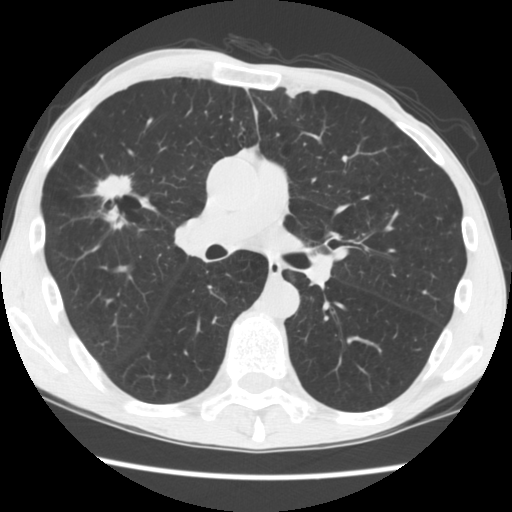
Axial slice from a low-dose chest CT screening exam. Second annual screen. Lung window (W 1500 / L -600 HU). Standard (soft-tissue) reconstruction kernel (STANDARD). 512 × 512 image matrix. Male participant, aged 56 years at enrolment. Current smoker at enrolment.
Expert-annotated lung lesion, bounding box (x1, y1, x2, y2) in pixels: (86, 164, 146, 231). The screening reader recorded 2 non-calcified nodules or masses ≥4 mm on this exam (right upper lobe, left upper lobe); which of them this box marks is not recorded. Official screen result: positive, change unspecified: nodule(s) >= 4 mm or enlarging nodule(s), mass(es), or other non-specific abnormalities suspicious for lung cancer.